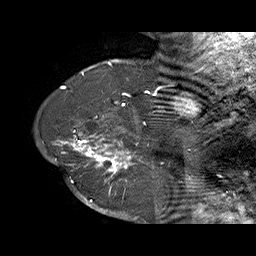
Breast MRI (dynamic contrast-enhanced), one sagittal slice. Slice 55 of 70 in the series (ordered by position). Dynamic contrast-enhanced series, time point 2 of 6 at this slice position (early post-contrast). 1.5 T. TE 4.5 ms, TR 32.4 ms. 3 mm slice thickness. 256 × 256 image matrix, field of view 180 × 180 mm. Female patient. Case-level facts recorded for this patient, not image findings: setting: breast cancer imaged before/during neoadjuvant chemotherapy; receptor status: HR-positive, HER2-negative.
Outlined on this slice (semi-automatically segmented with operator editing):
- analysis volume of interest (the breast-tissue region the enhancement analysis was run in; not a lesion): bounding box [x1, y1, x2, y2] px = [71, 128, 159, 202]
- tumour enhancement mask (voxels above the 100 % enhancement threshold inside the analysis volume of interest): [71, 130, 149, 202]